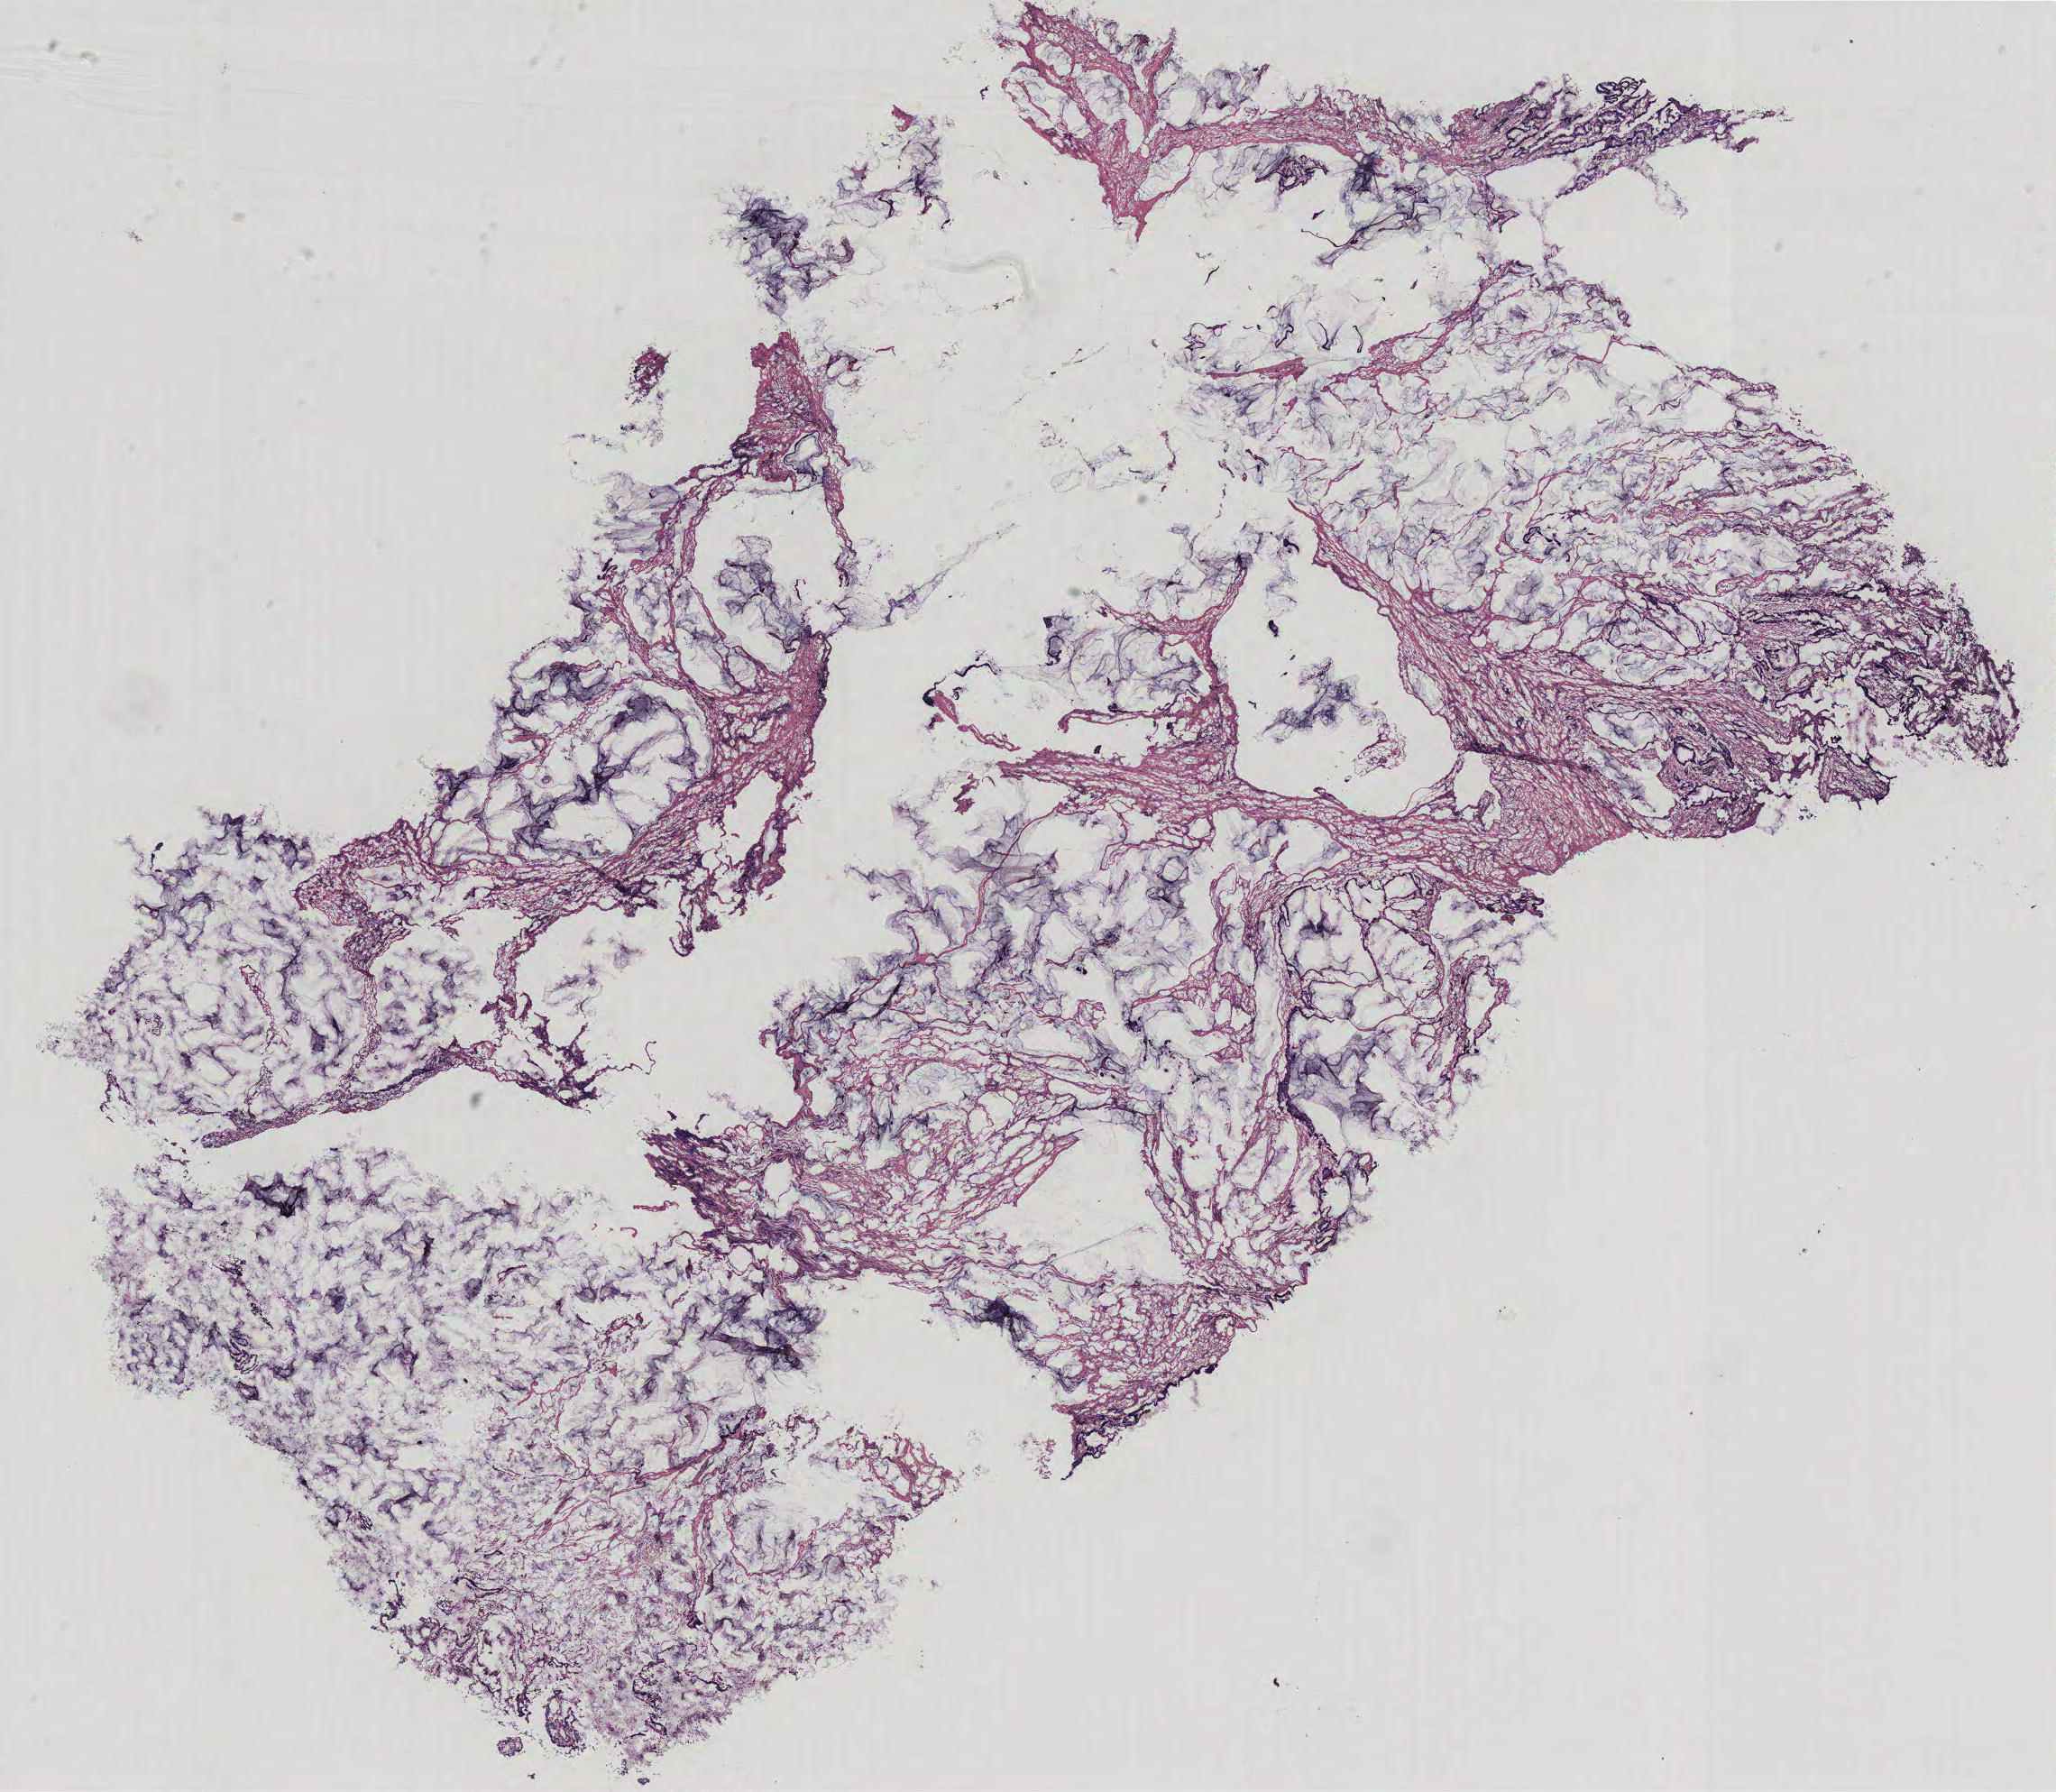
Whole-slide histology image, Hematoxylin and eosin (H&E) stained, a low-resolution overview of the entire scanned area, about 18.2 x 15.9 mm (slide scanned at 40x). Colon, tissue type not recorded.
Patient diagnosis (cohort enrolment): colon cancer (colon).